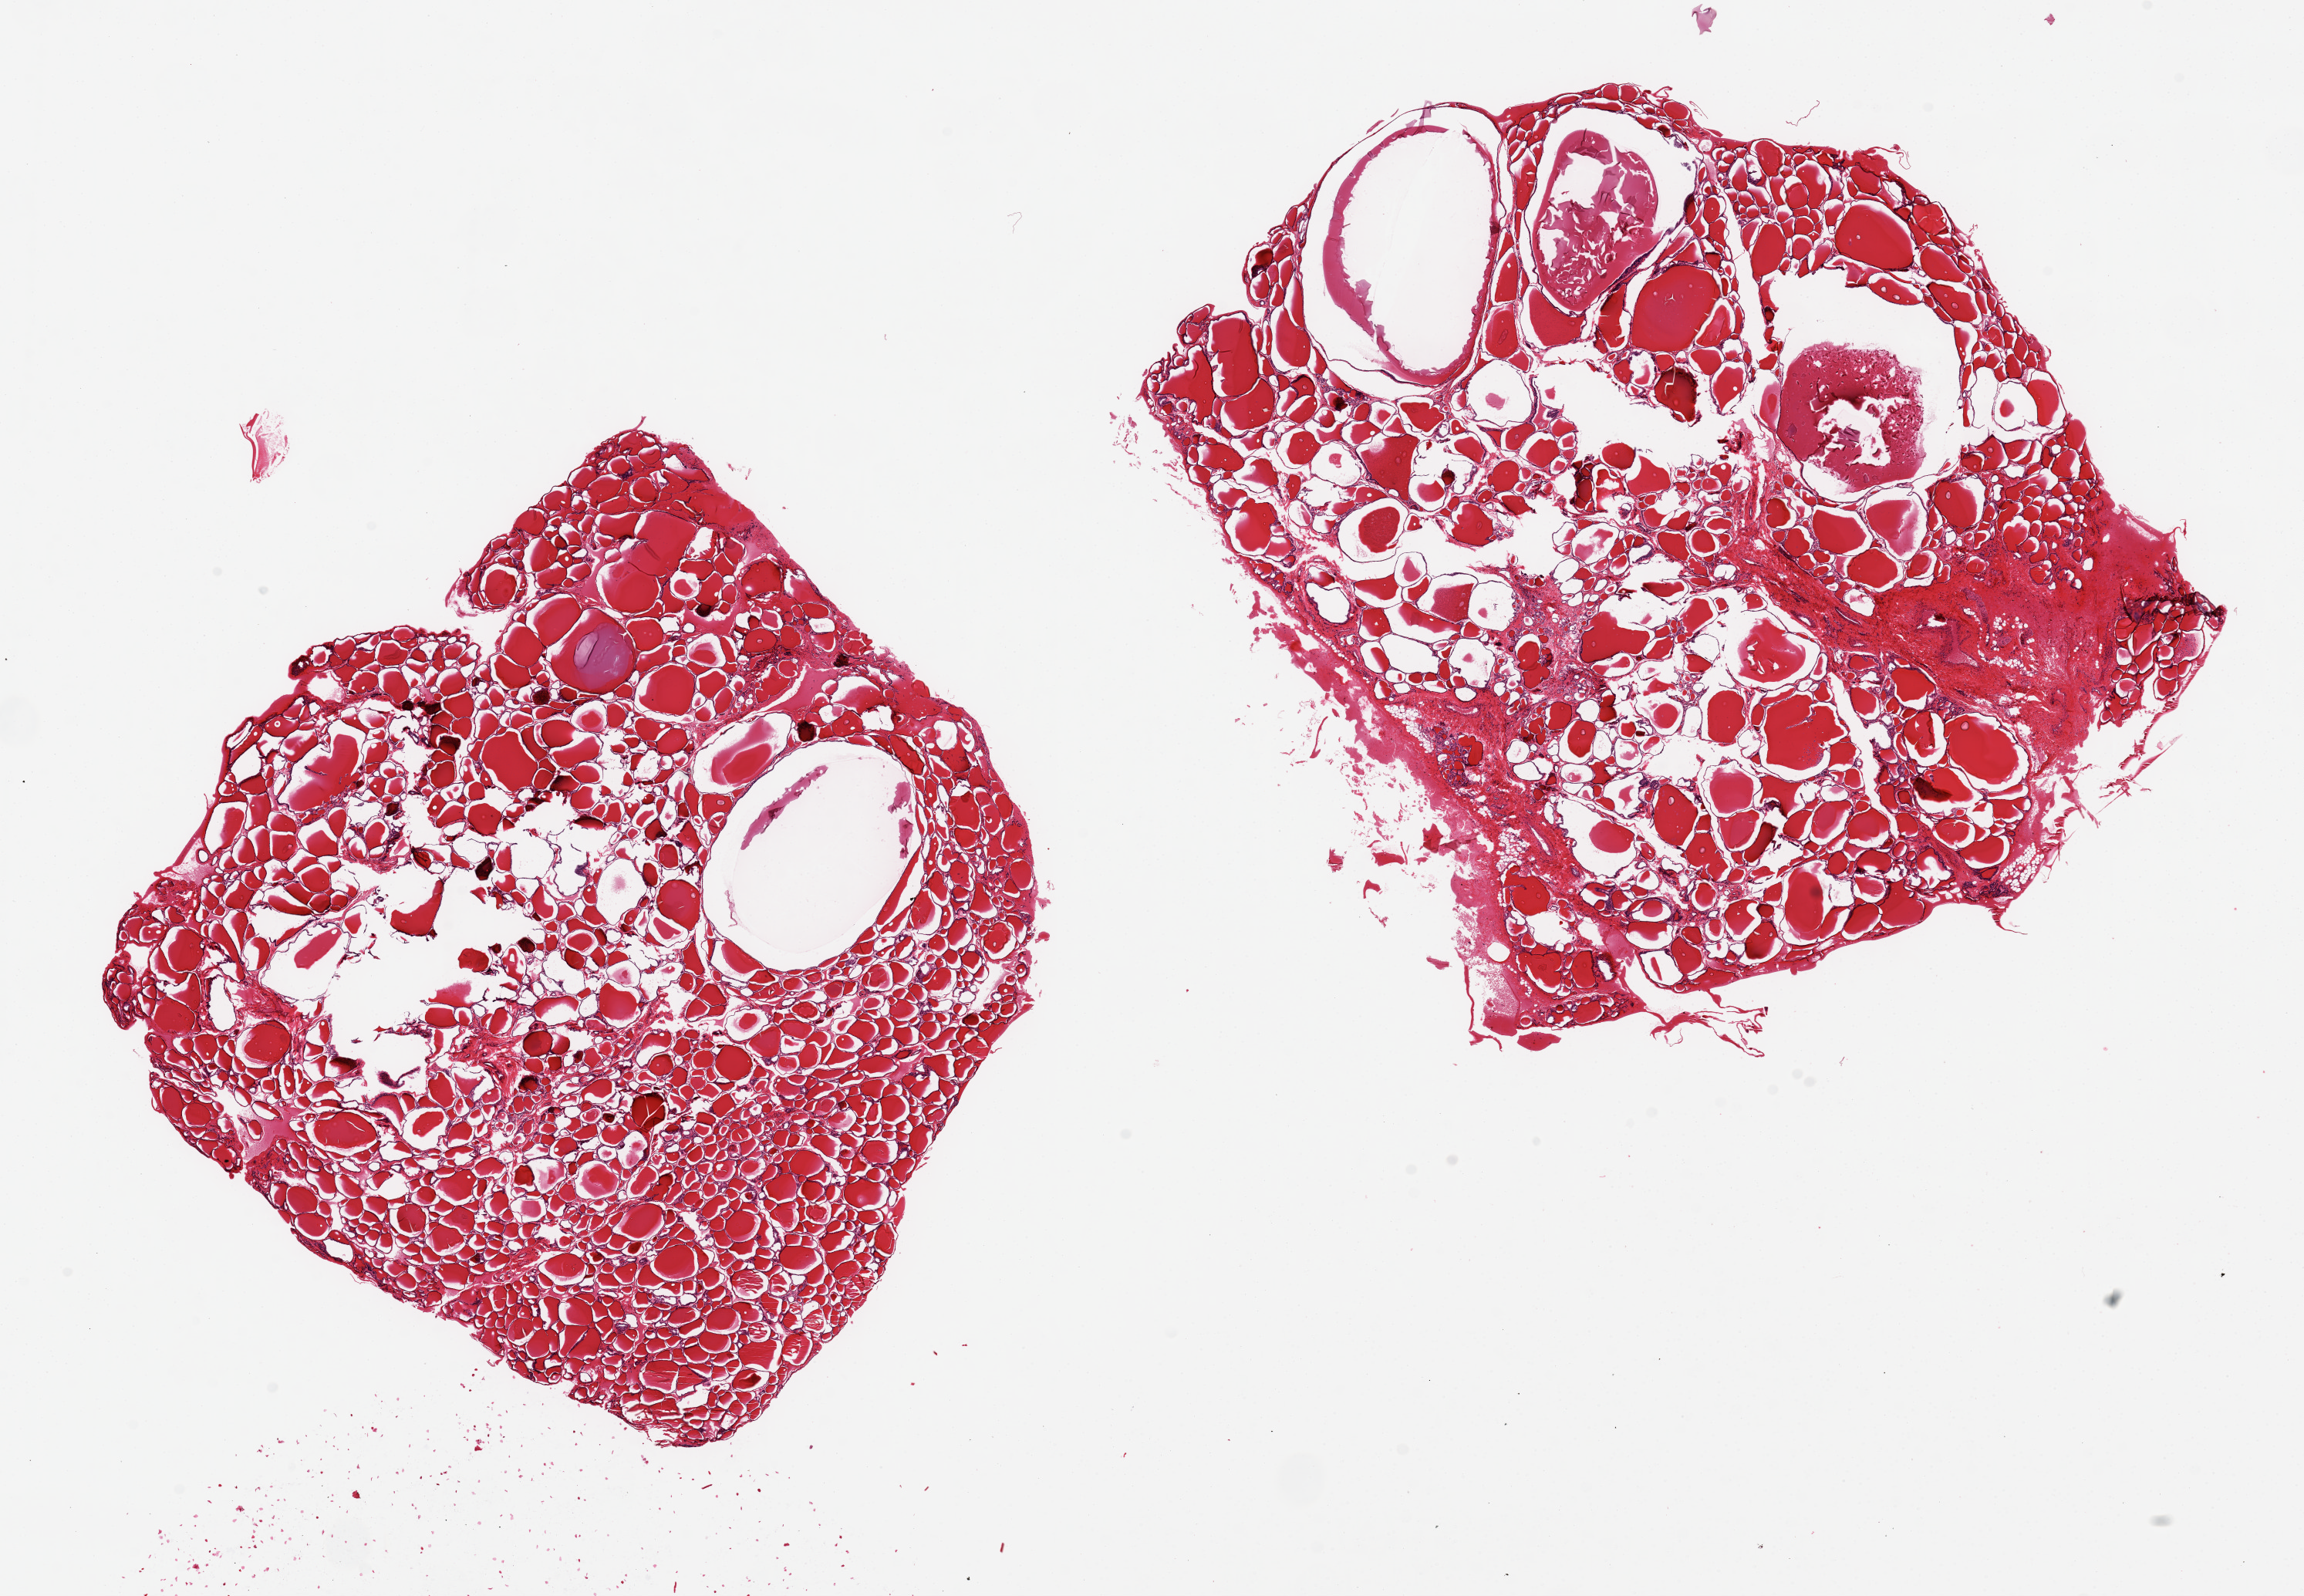
Hematoxylin and eosin (H&E) whole-slide image, brightfield — low-resolution overview of the scanned area, about 23.6 x 16.4 mm, PAXgene-fixed paraffin-embedded (PFPE) section, target tissue: thyroid, tissue donor sample. Donor sex: female.
* pathologist's review note for this sample: 2 pieces, 8x8mm, 9x9mm; several cystic follicles